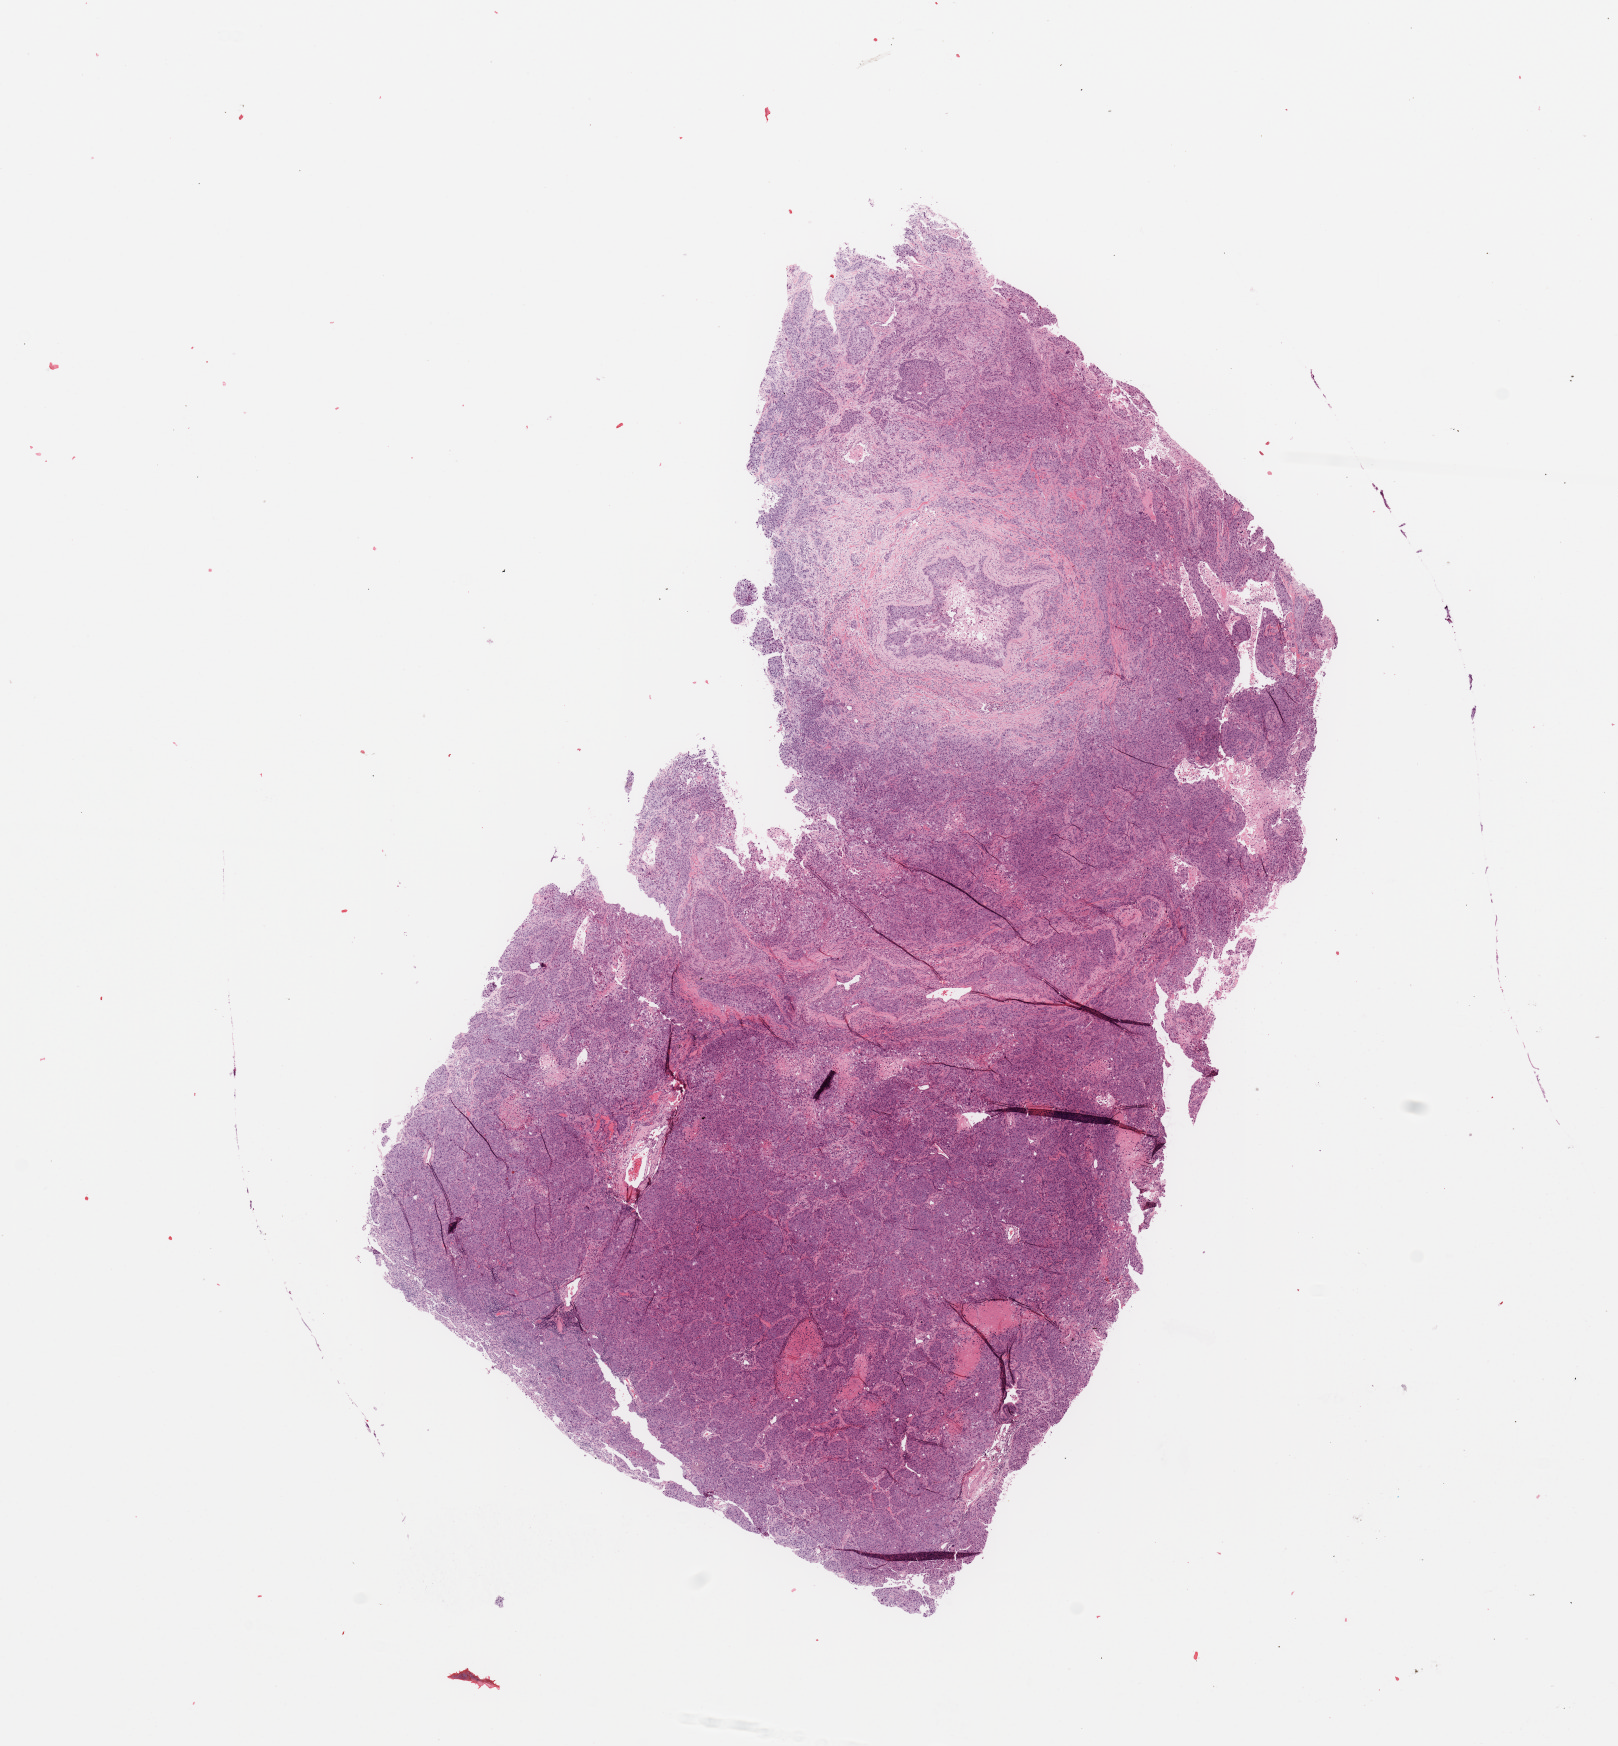
Digitized H&E-stained tissue section (whole slide) — shown as a low-resolution overview of the whole scanned area (about 12.8 x 13.8 mm, from a 20x scan); lung, tumour tissue. Patient: female, age 53 years. Histologic grade: G3 (poorly differentiated).
• AJCC pathologic stage: IIIA
• diagnosis: Adenocarcinoma, NOS
• primary tumour site (as recorded): right lower lobe